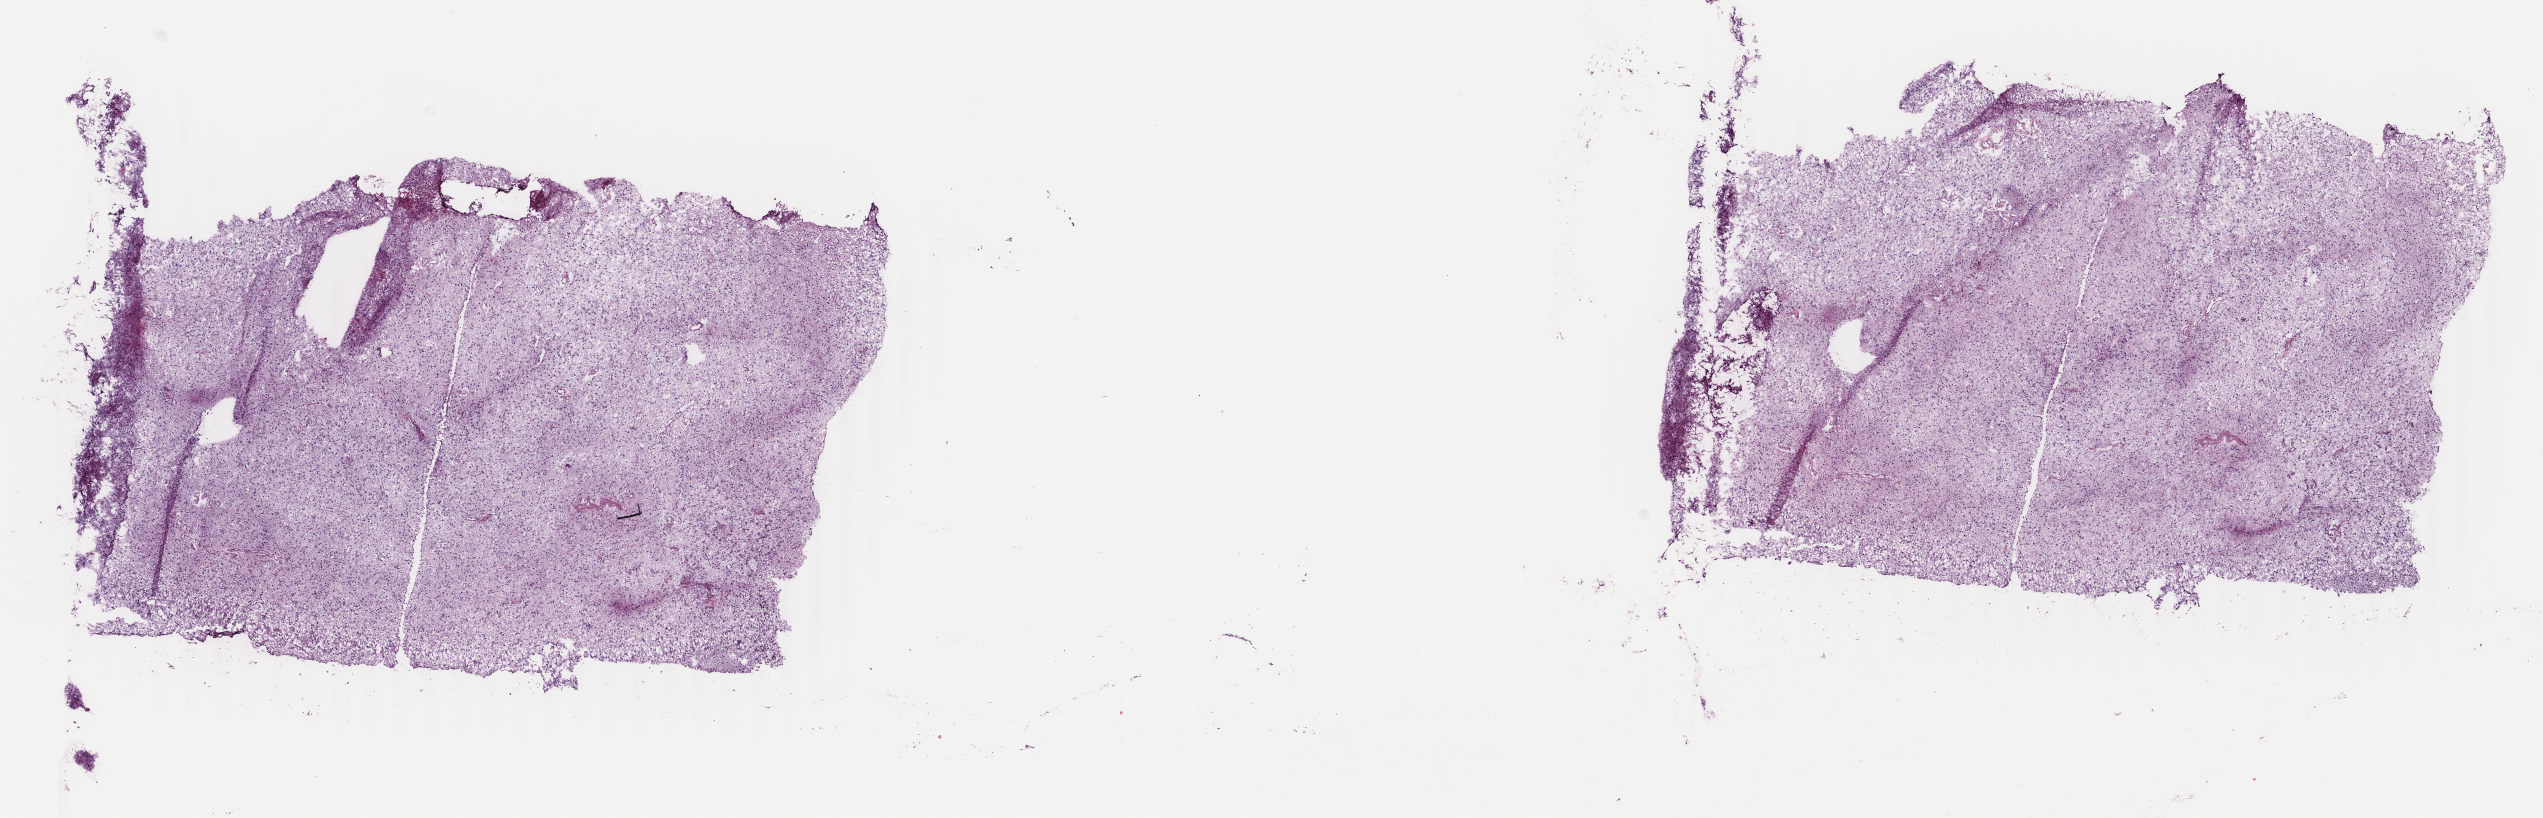
Digitized H&E tissue section (whole slide), shown as a low-resolution overview of the whole scanned area (about 20.2 x 6.5 mm, acquisition: 40x scan); frozen section from the top of the tissue portion; sample: primary tumour, brain. Male, age 46 years at initial diagnosis. Histologic grade: G3 (poorly differentiated). Slide review estimates, as recorded: tumour cells 45%, tumour nuclei 90%, normal cells 5%, stromal cells 50%, necrosis 0%. Inflammatory infiltration, as recorded: lymphocyte infiltration 0%, monocyte infiltration 0%, neutrophil infiltration 0%.
Diagnosis: Astrocytoma, anaplastic (cerebrum).